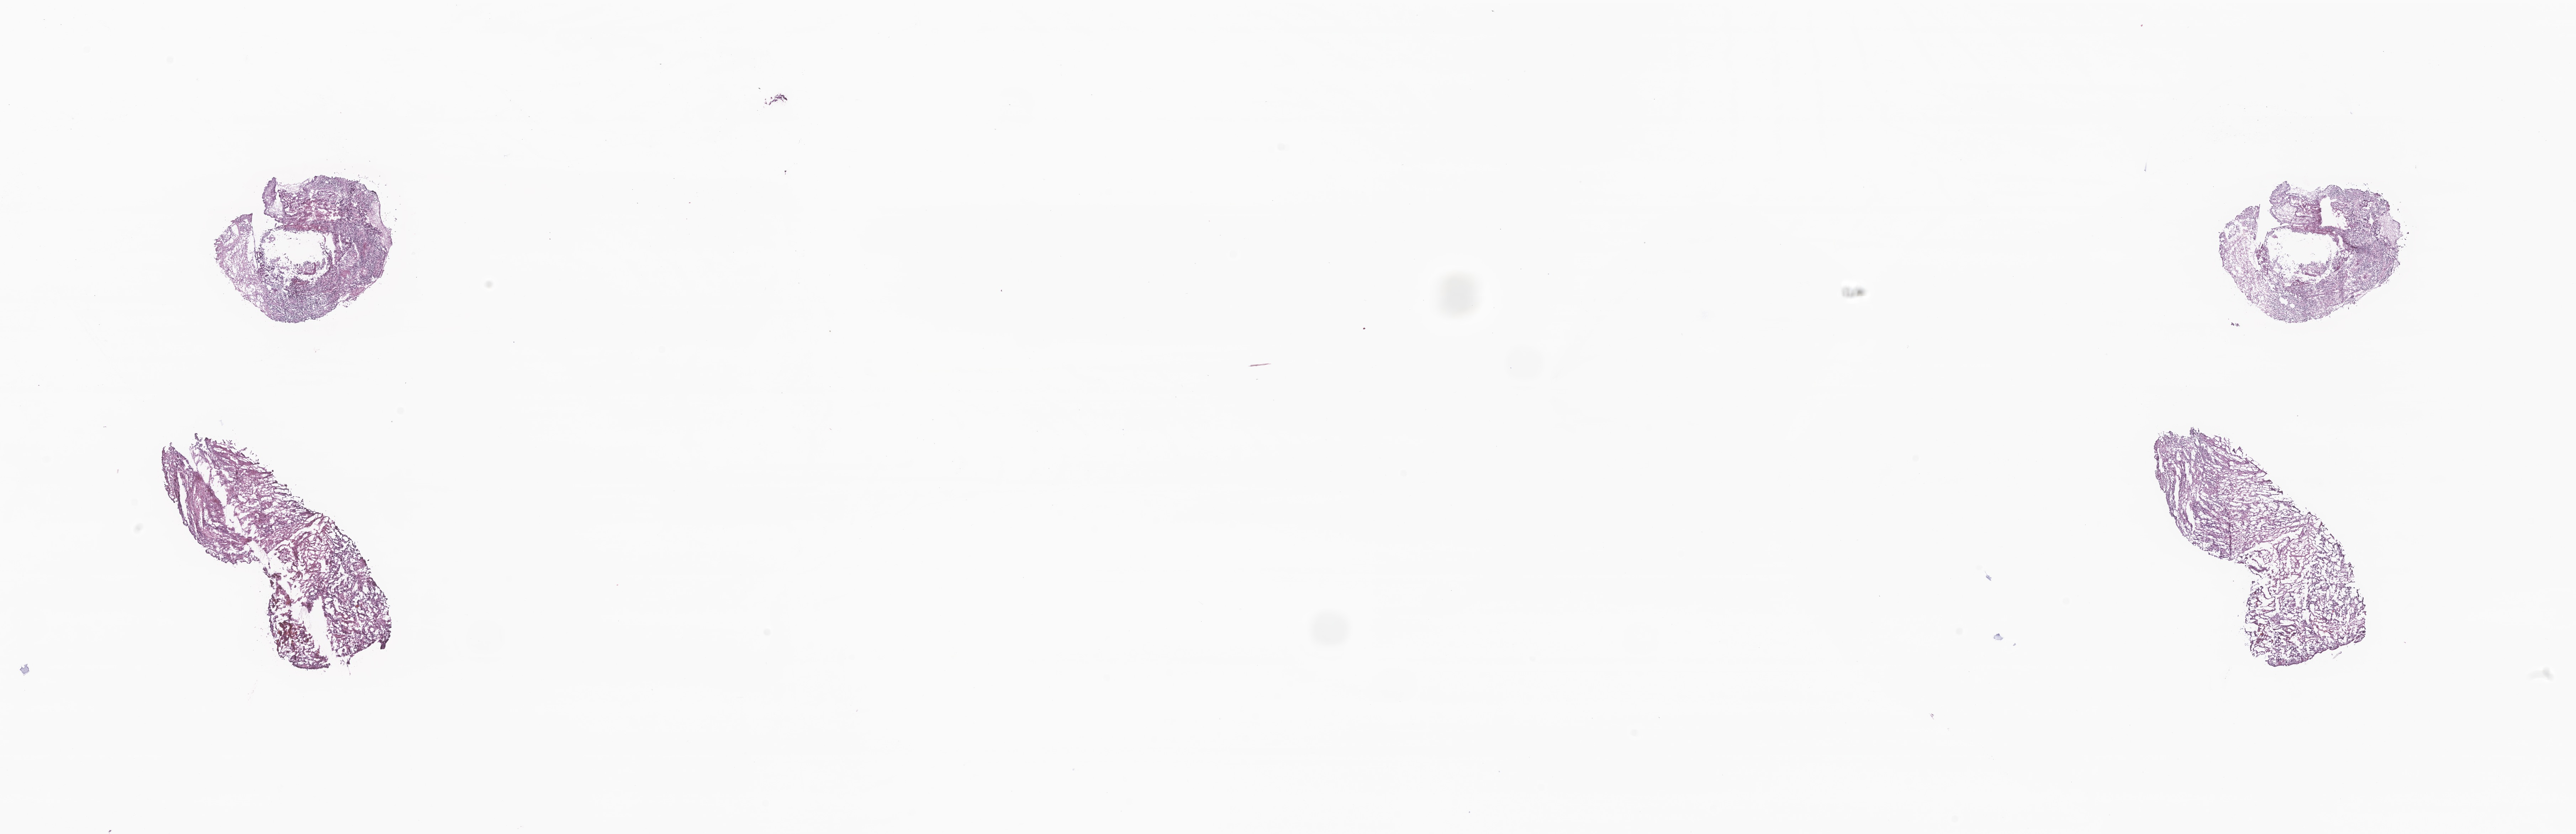
Whole-slide image, haematoxylin and eosin stain of tumor tissue from the brain, shown as a low-resolution overview of the whole scanned area (about 30.5 x 9.9 mm); frozen section (OCT-embedded). Patient female; age 469 days (about 1.3 years).
Recorded diagnosis: Medulloblastoma, NOS.